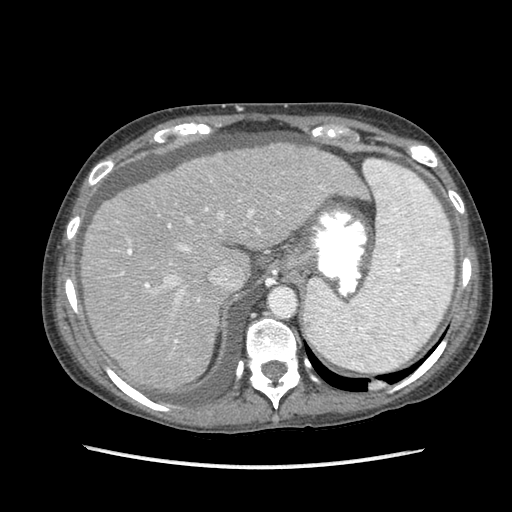
Contrast-enhanced abdominal CT (liver protocol), one axial slice; slice 67 of 87 in the series (ordered by position); reconstruction kernel STANDARD; soft-tissue window (W 400 / L 40 HU); 2.5 mm slice thickness; 512 × 512 image matrix, field of view 340 × 340 mm. Case-level facts recorded for this patient, not image findings: diagnosis: hepatocellular carcinoma (patient treated with transarterial chemoembolisation; whether this scan precedes or follows treatment is not stated here); TNM stage (as recorded): Stage-IIIB; Child-Pugh class: A; tumour differentiation: no biopsy; tumour nodularity: uninodular.
Outlined on this slice (semi-automatically segmented with operator editing):
- liver parenchyma outside the tumour (the mass and vessels are separate outlines, so this box may not span the whole liver): bounding box (x1, y1, x2, y2) in pixels: (82, 142, 364, 389)
- liver vessels: (120, 186, 323, 343)